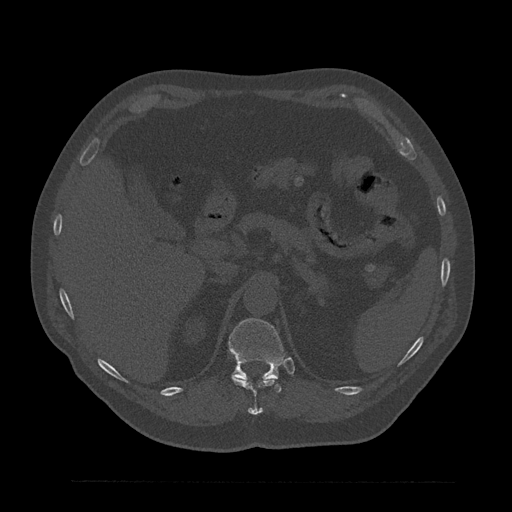
CT including the spine, one axial slice. Position 258 of 797 along the scan axis. Reconstruction kernel Br40s/3. 120 kVp. Bone window (W 1800 / L 400 HU). 512 × 512 image matrix. Male patient, age 61 years. Case-level facts recorded for this patient, not image findings: primary cancer: prostate.
Annotated regions visible in this slice (semi-automatically segmented with operator editing):
- T11 vertebra: box from (x=232, y=376) to (x=277, y=415) px
- T12 vertebra: (x=229, y=318)–(x=284, y=393)